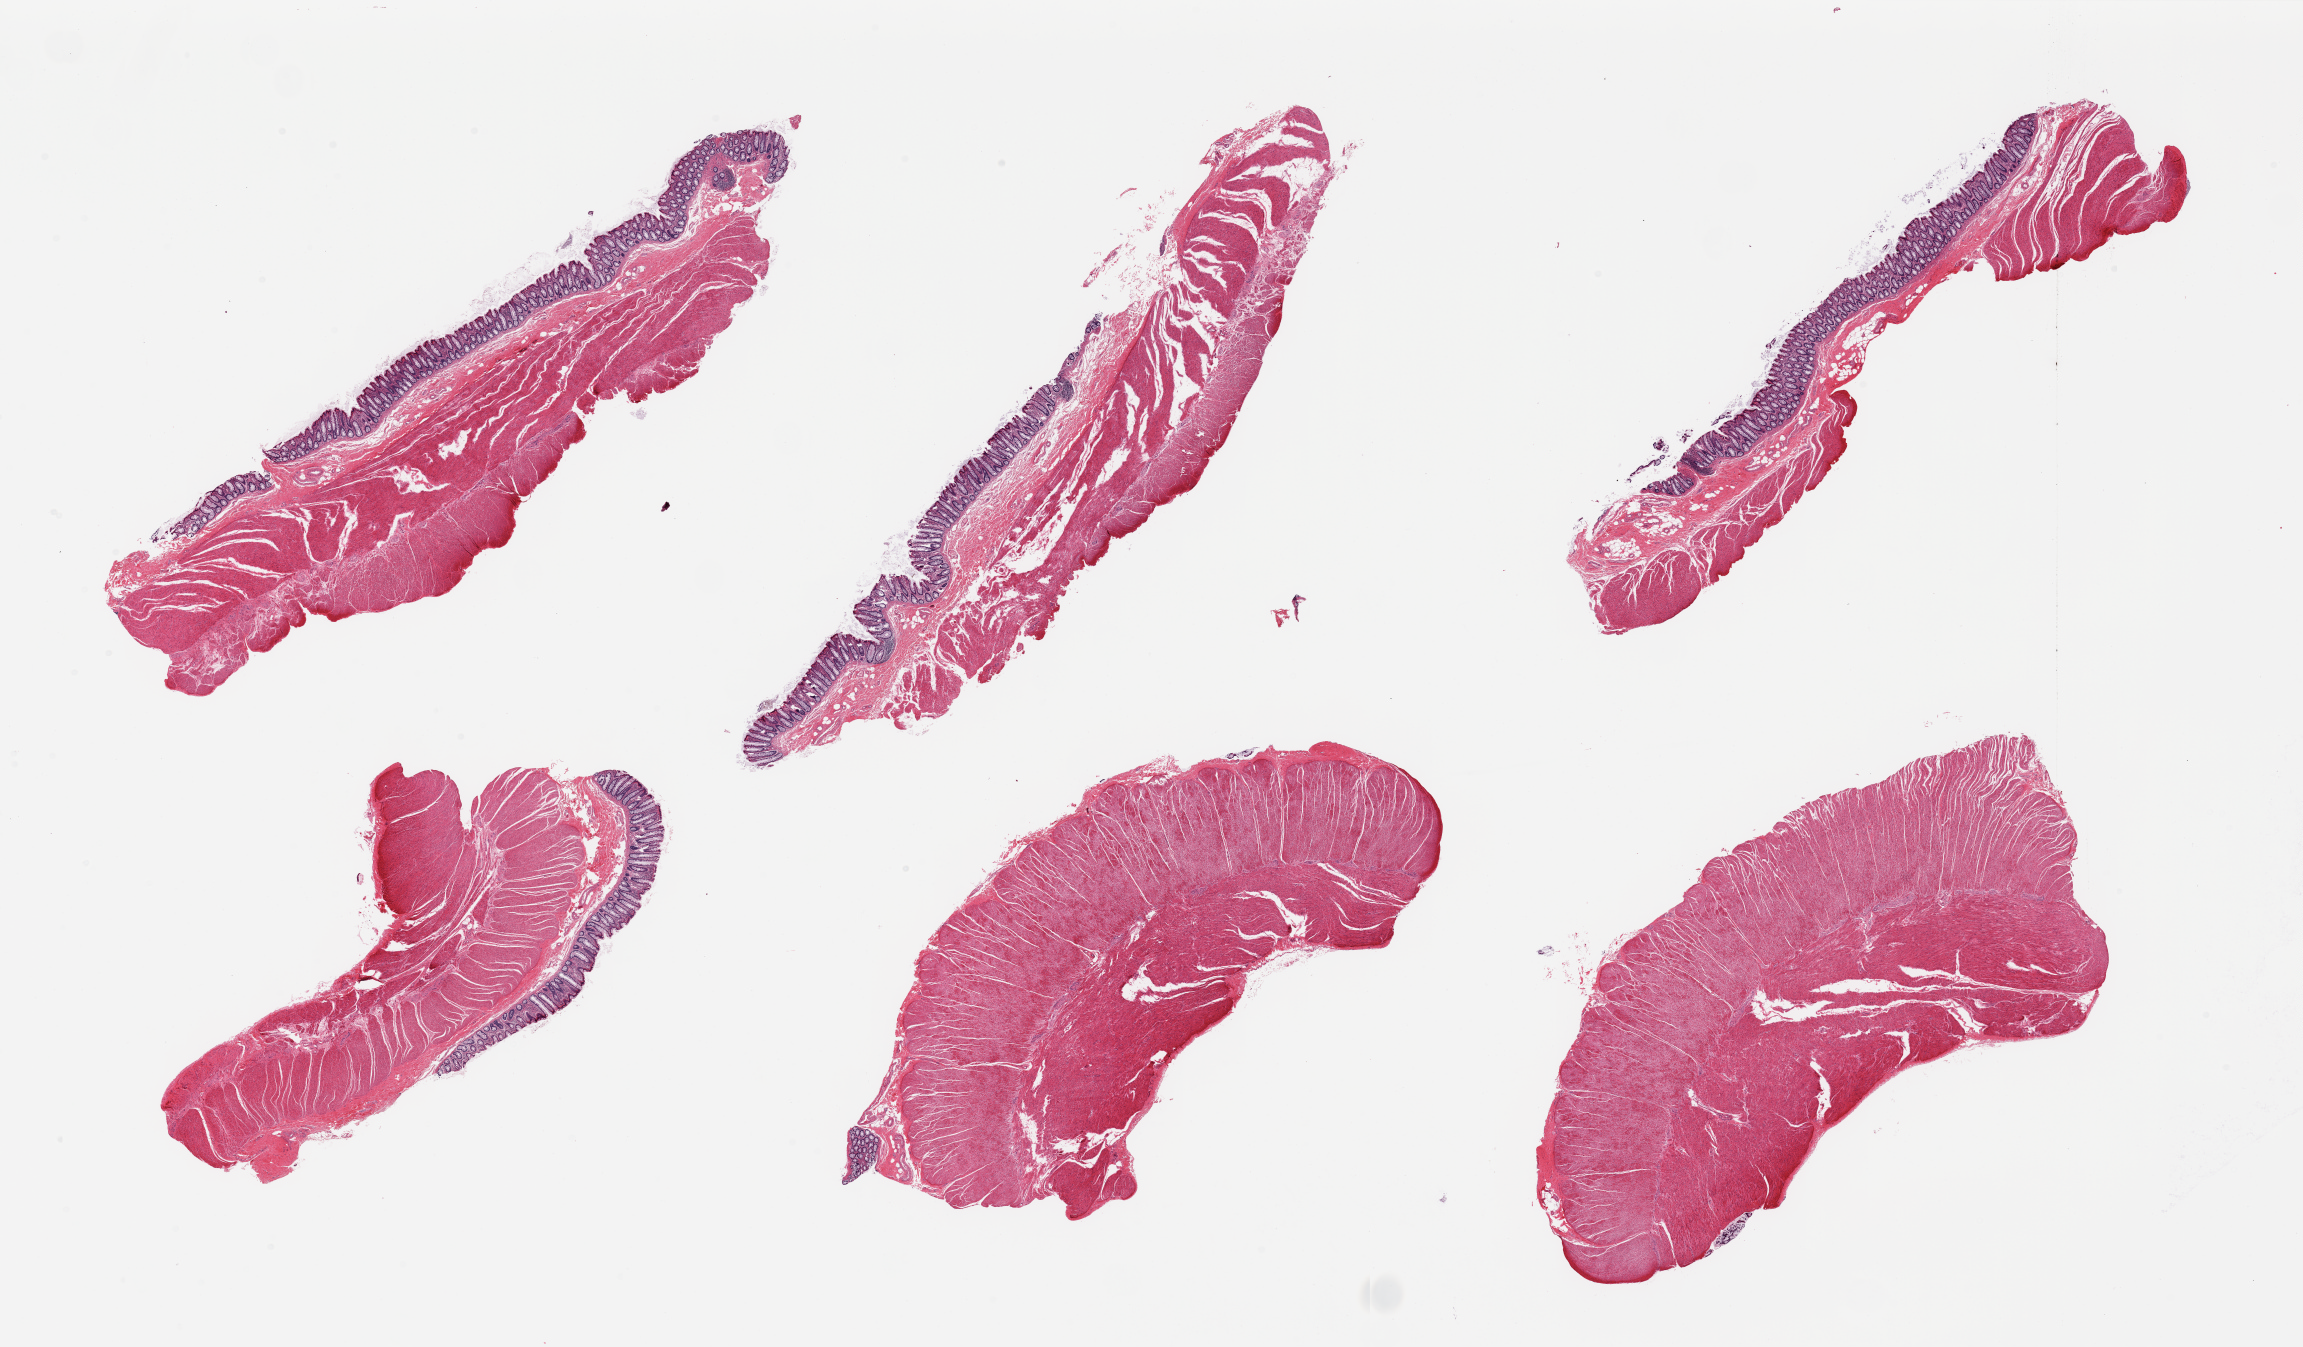
Whole-slide image, H&E stain, shown as a low-resolution overview of the whole scanned area (about 36.4 x 21.3 mm). PAXgene-fixed, paraffin-embedded tissue. Section of sigmoid colon (target tissue). Donor tissue sample.
Review note (as recorded): 6 pieces; 4 contain mucosa (NOT target); all contain muscularis.